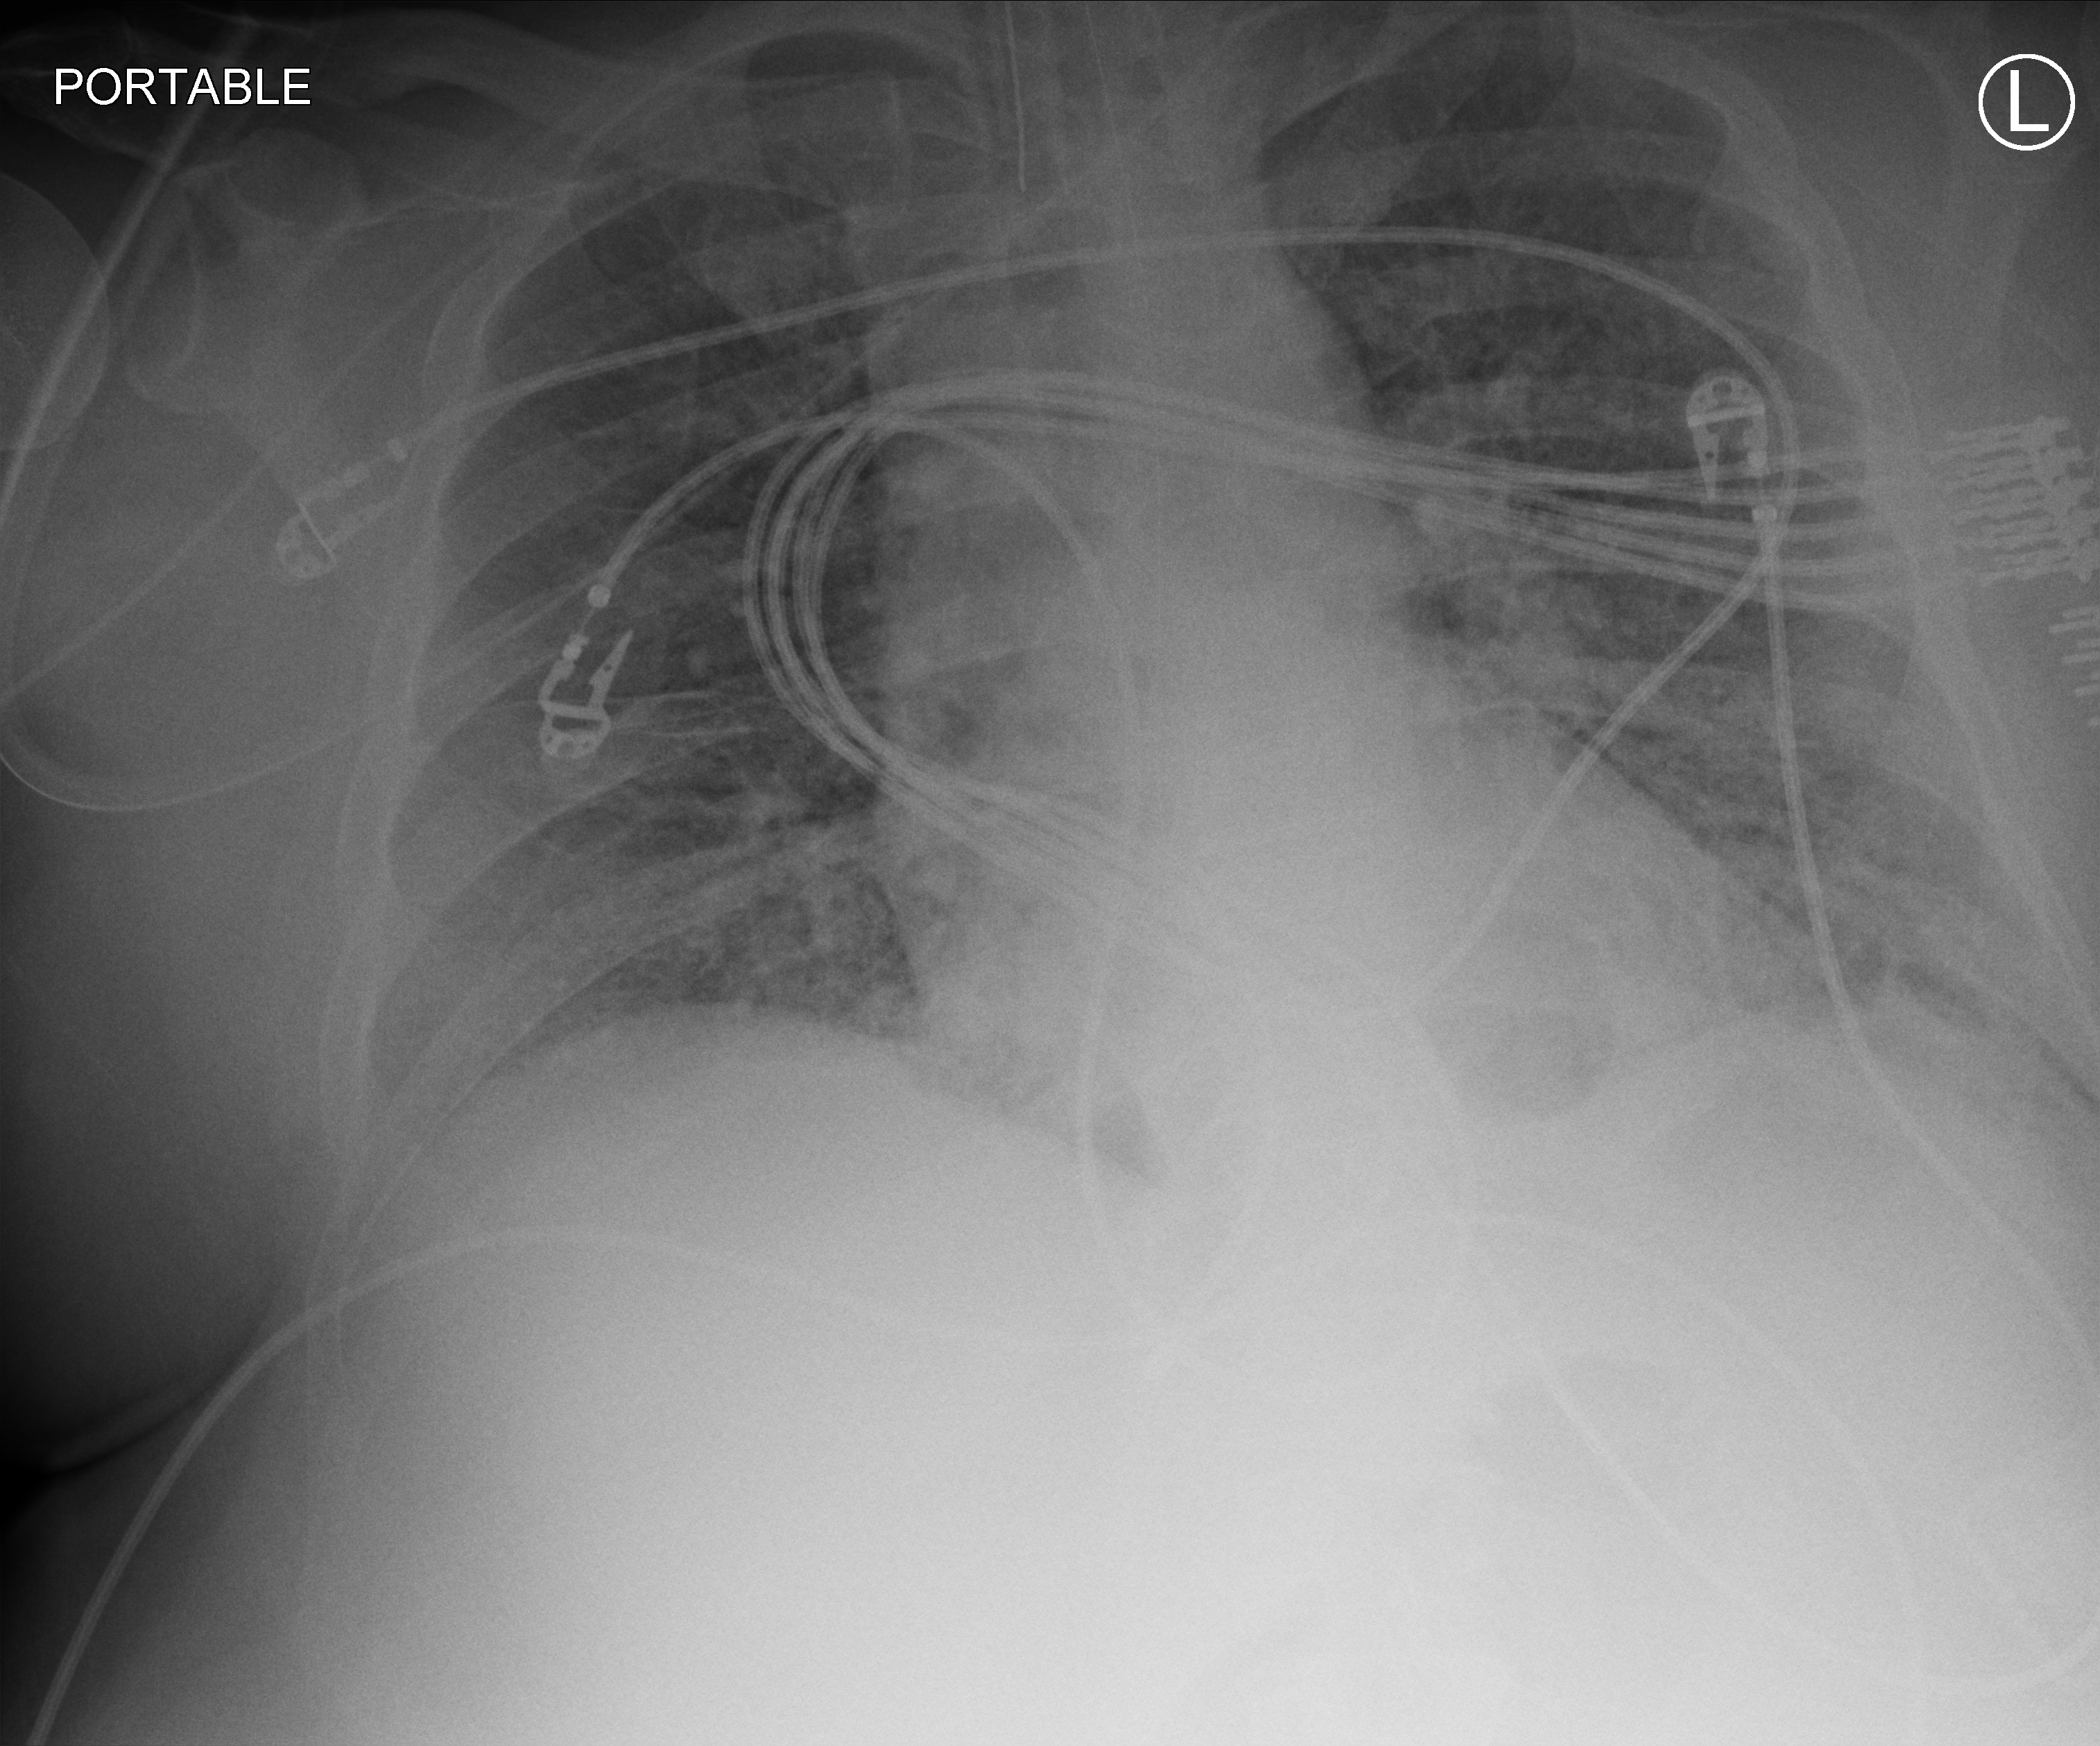
Bedside chest radiograph (computed radiography), anteroposterior (AP) projection. Adult patient hospitalised with COVID-19, age 18–59 years.
Admission-level facts for this patient (not findings on this image; timing relative to this image not recorded): length of hospital stay: 26 days; mechanically ventilated during this hospital stay: yes; other chronic lung disease (admission record): no.